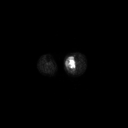
FDG PET of an extremity soft-tissue mass (from a PET/CT study), one axial slice; slice 139 of 223 in the series (ordered by position); 3.27 mm slice thickness; 128 × 128 image matrix, field of view 700 × 700 mm. Patient: female, 70 years. Case-level facts recorded for this patient, not image findings: histological type: extraskeletal high grade osteogenic sarcoma; grade: high; site of the primary tumour: left calf.
Outlined on this slice (expert contour drawn on MRI and transferred to this co-registered scan by the dataset authors):
- gross tumour volume (mass): bounding box (x1, y1, x2, y2) in pixels: (66, 58, 75, 70)